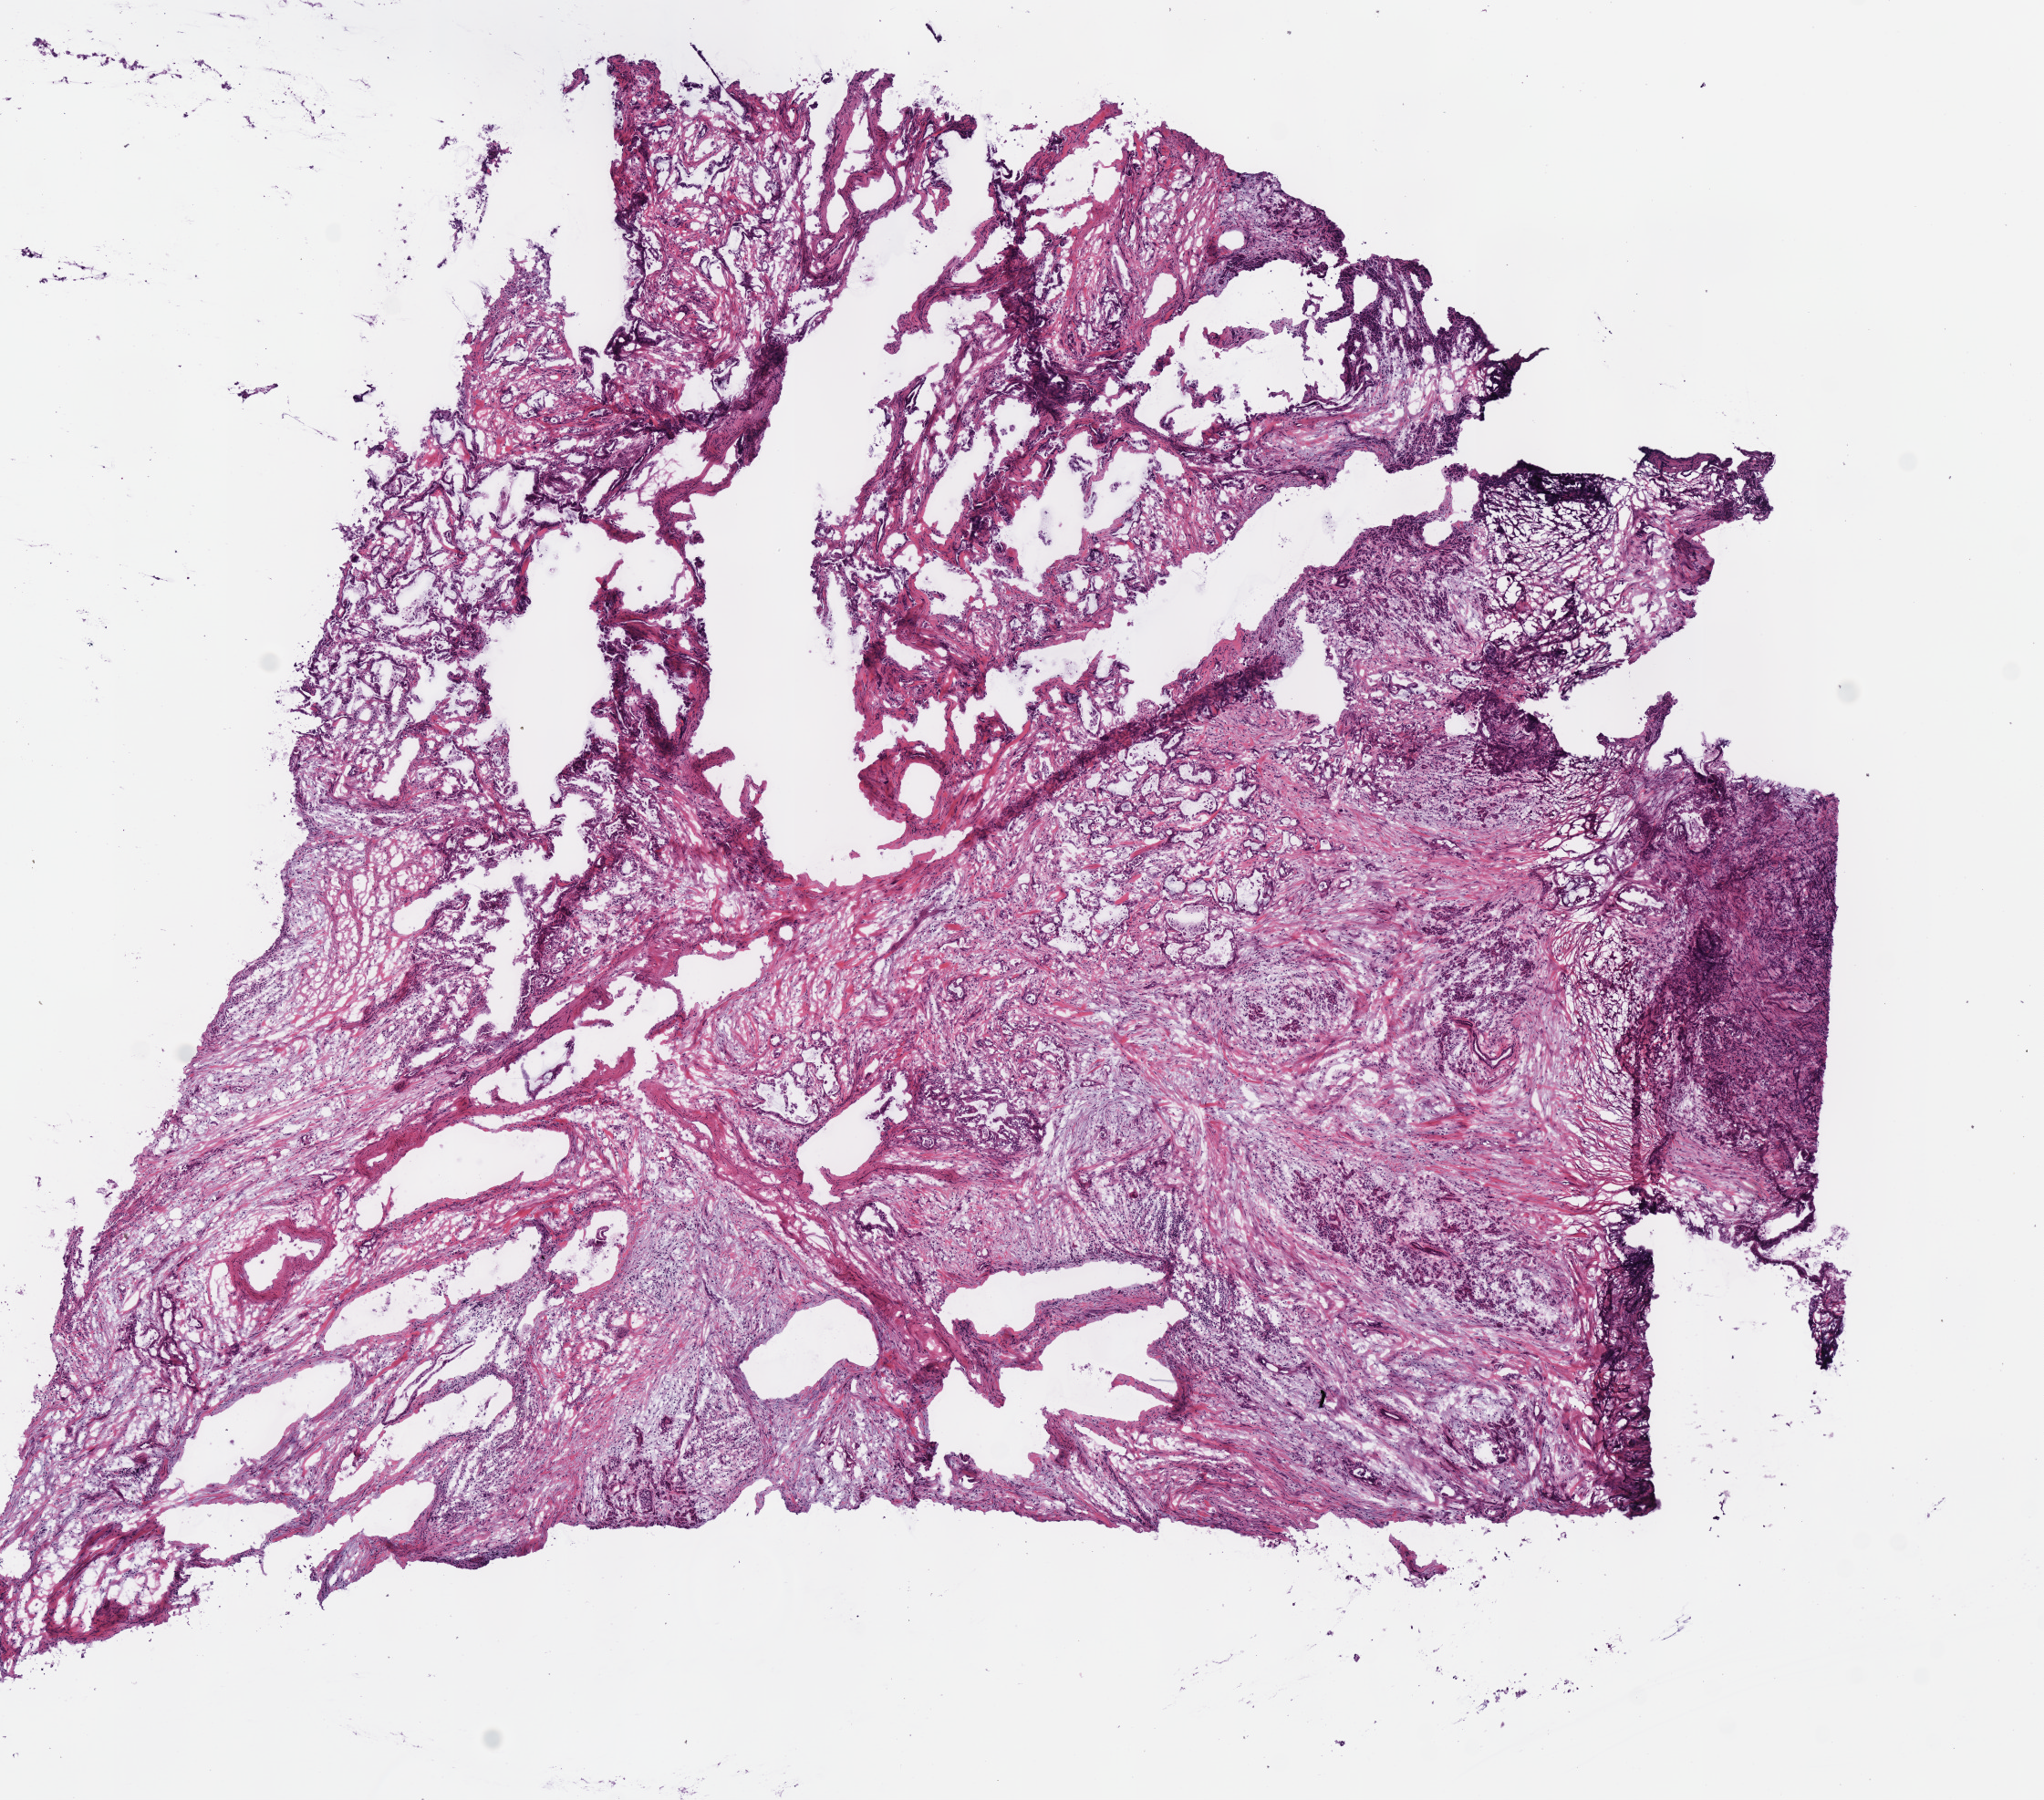
Whole-slide histology image, H&E, whole scanned area (about 8.8 x 7.8 mm, from a 40x scan) shown as a low-resolution overview. Frozen section from the bottom of the tissue portion. Sample: primary tumour, pancreas. Female patient; age at initial diagnosis 73 years. Histologic grade: G2 (moderately differentiated). Composition of this section per pathologist review: tumour cells 74%, tumour nuclei 53%, normal cells 13%, stromal cells 13%, necrosis 0%. Inflammatory infiltration, as recorded: lymphocyte infiltration 15%, monocyte infiltration 5%, neutrophil infiltration 15%.
Diagnosis: Infiltrating duct carcinoma, NOS (head of pancreas). AJCC pathologic stage: IIB (6th edition). Lymph nodes positive (case pathology): 5 of 13 examined.